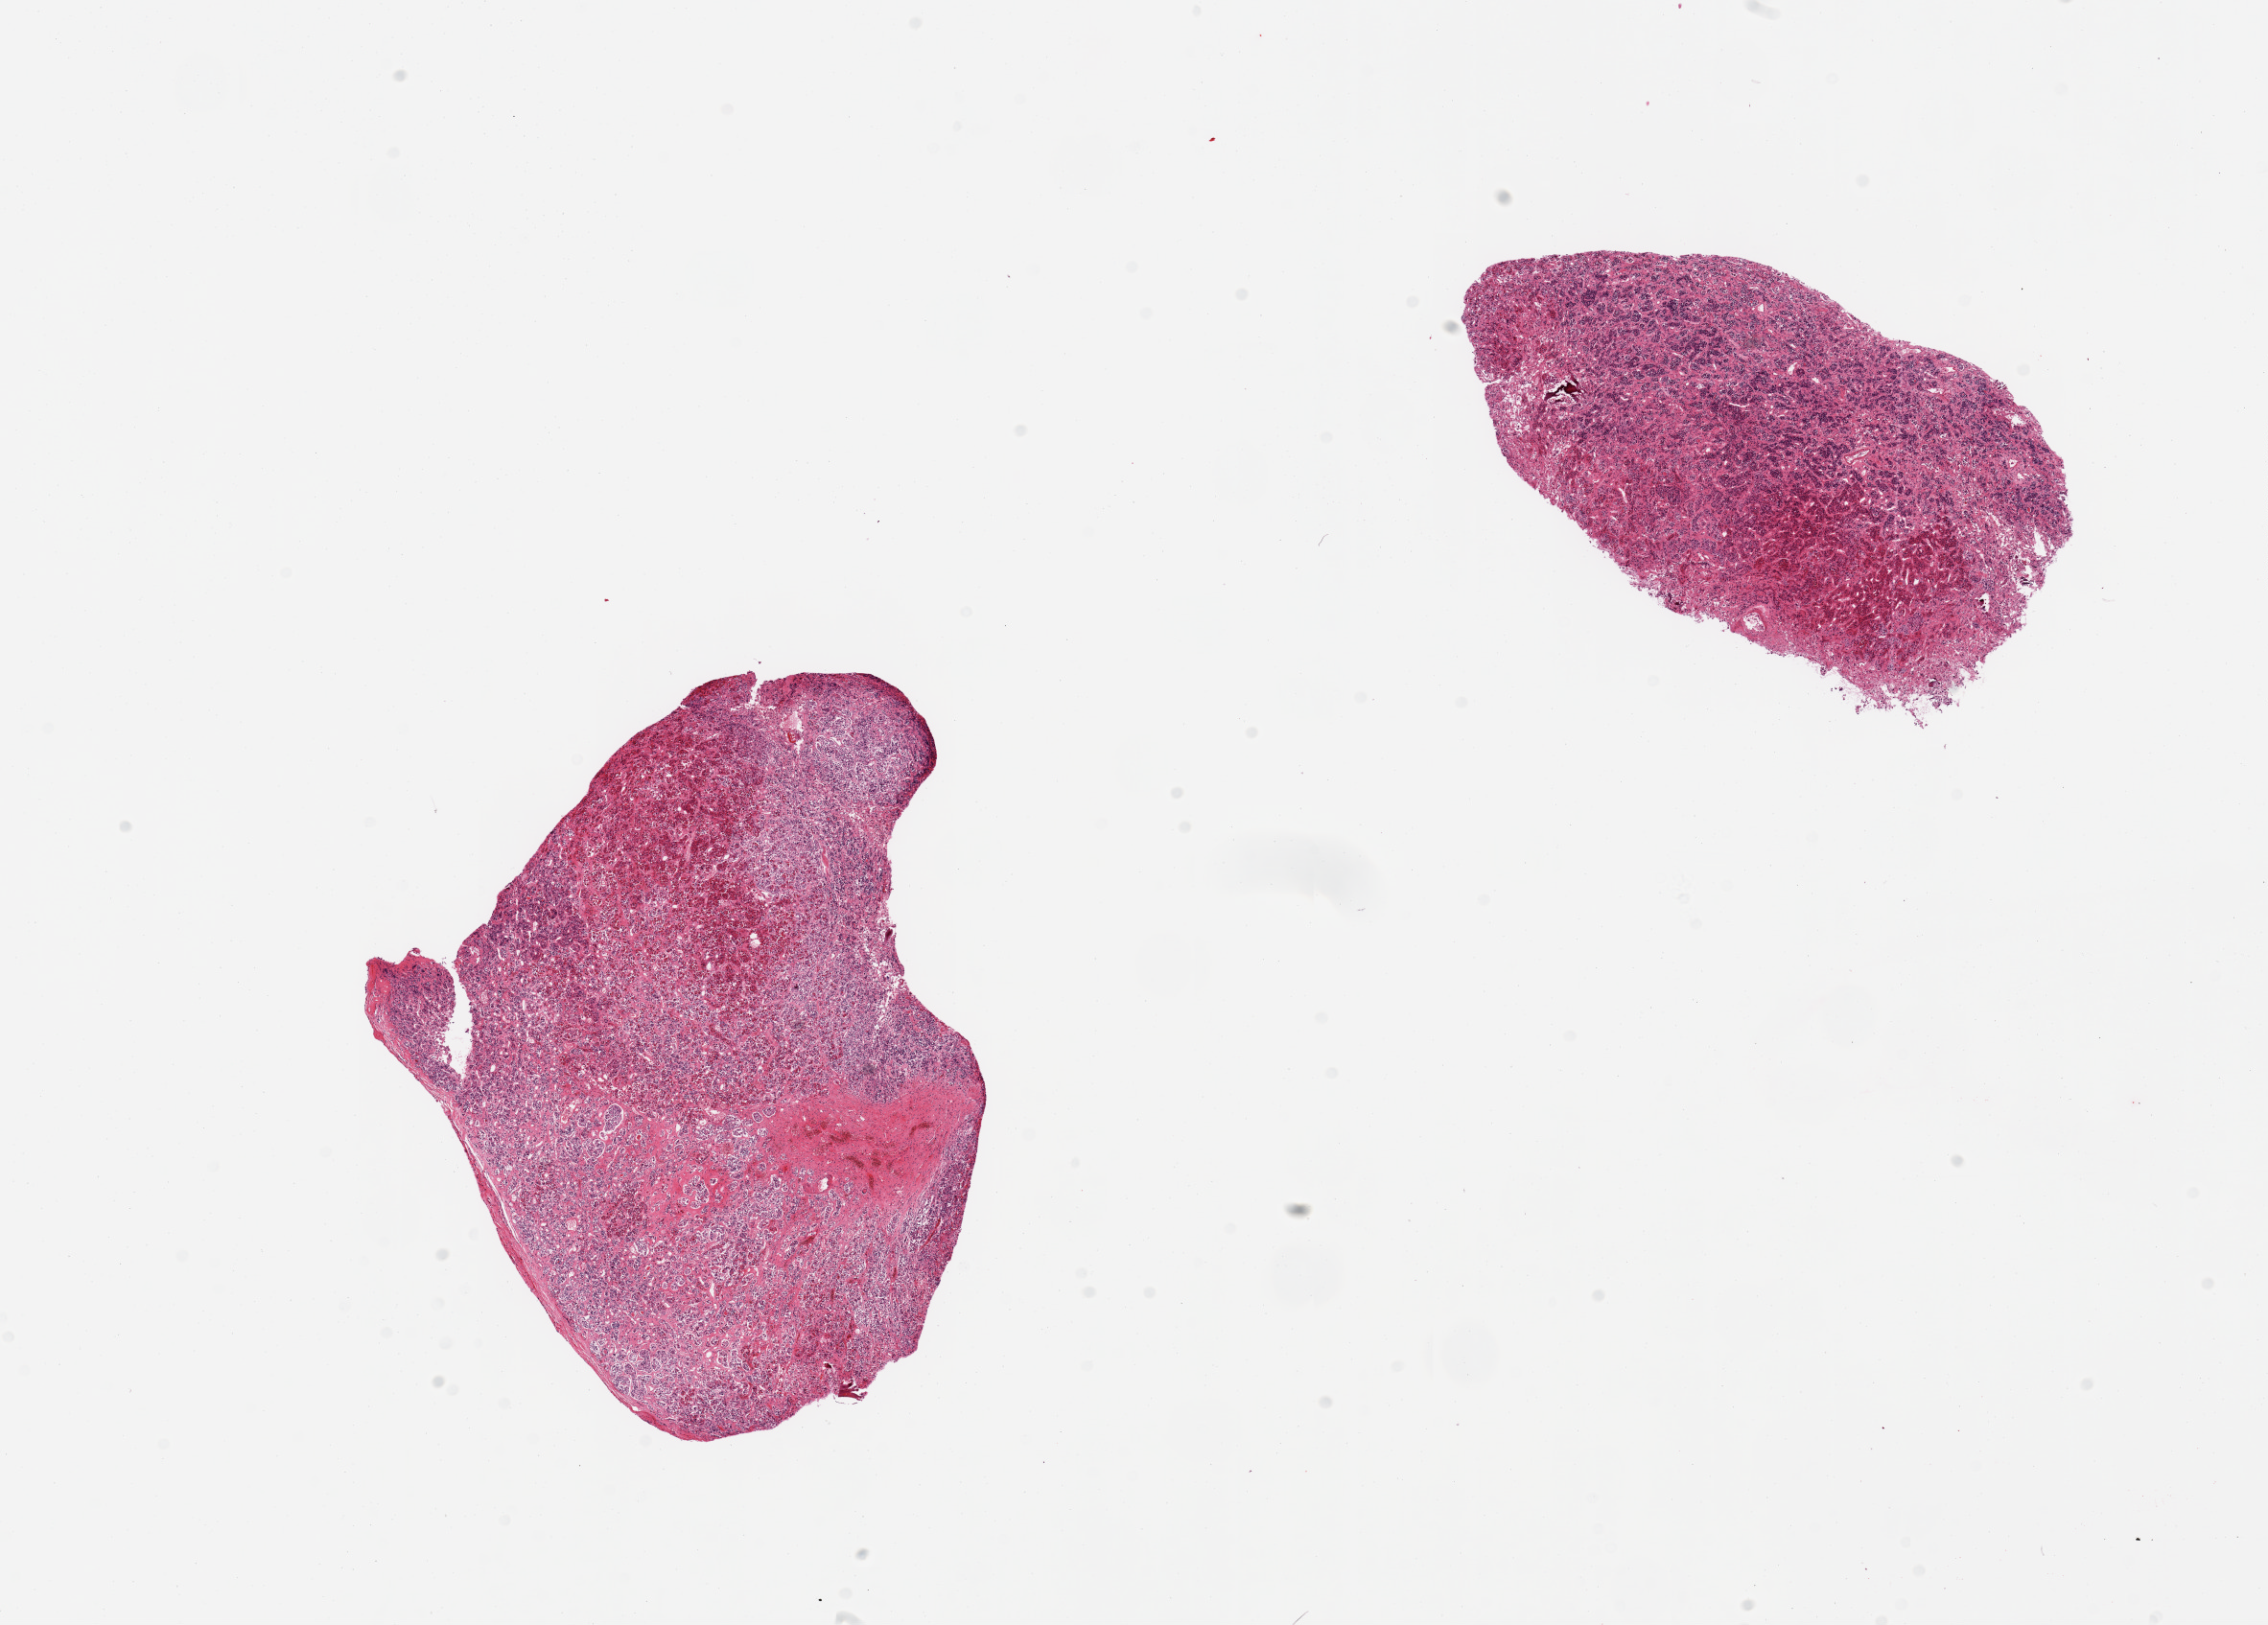
Whole-slide image, H&E stain — a low-resolution overview of the entire scanned area, about 18.7 x 13.4 mm. PAXgene-fixed paraffin-embedded (PFPE) section. Sampled site (target tissue): pituitary. Tissue donor sample.
Review note (as recorded): 2 pieces, moderately-markedly autolyzed adenohypophysis.